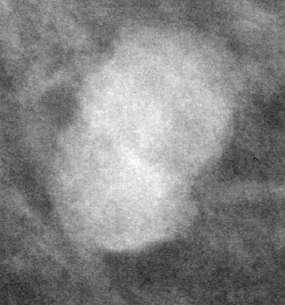
Cropped region of a digitized screen-film mammogram centred on a radiologist-marked abnormality; right breast; CC view.
Finding: mass, shape lobulated, margins circumscribed / ill defined; BI-RADS assessment category 4; subtlety rating 5 on a 1 (subtle) to 5 (obvious) scale; pathology result (as recorded, not read from the image): malignant.